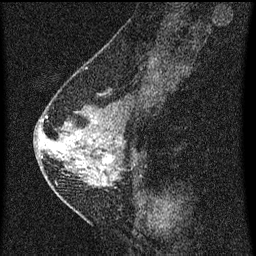
Breast MRI (dynamic contrast-enhanced), one sagittal slice; slice 26 of 60 in the series (ordered by position); dynamic contrast-enhanced series, image 2 of 3 at this slice position (ordered by acquisition); 1.5 T; TE 4.2 ms, TR 8 ms; 2 mm slice thickness; 256 × 256 image matrix. Female patient, age 47 years.
Outlined on this slice (semi-automatic segmentation, software-assisted and operator-edited):
- analysis volume of interest (the breast-tissue region the enhancement analysis was run in; not a lesion): bounding box (x1, y1, x2, y2) in pixels: (42, 92, 139, 199)
- tumour enhancement mask (voxels above the 70 % enhancement threshold inside the analysis volume of interest): (94, 122, 122, 171)